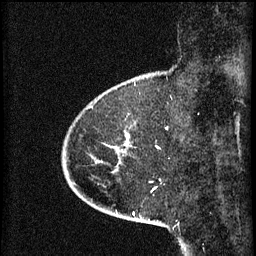
Breast MRI (dynamic contrast-enhanced), one sagittal slice. Position 13 of 60 along the scan axis. 3 images stored at this slice position (order not interpretable as contrast timing). 1.5 T. TE 4.2 ms, TR 8.2 ms. 2 mm slice thickness. 256 × 256 image matrix, field of view 200 × 200 mm. Female patient, age 45 years.
Outlined on this slice (semi-automatic segmentation, software-assisted and operator-edited):
- analysis volume of interest (the breast-tissue region the enhancement analysis was run in; not a lesion): box from (x=83, y=102) to (x=136, y=171) px
- tumour enhancement mask (voxels above the 70 % enhancement threshold inside the analysis volume of interest): (x=124, y=136)–(x=129, y=145)